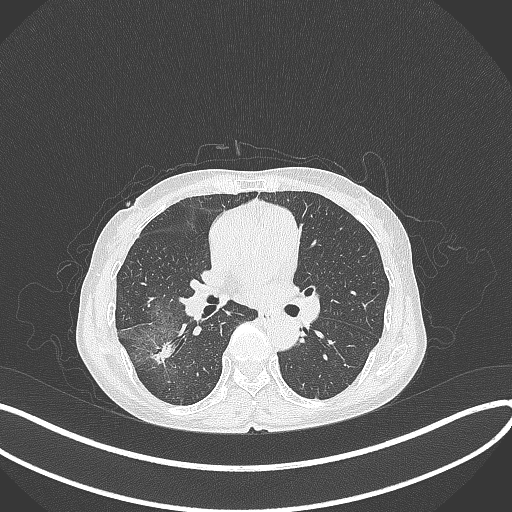
Chest CT, one axial slice. Slice 212 of 371 in the series (ordered by position). Reconstruction kernel B70f. 120 kVp. Lung window (W 1500 / L -600 HU). 1 mm slice thickness. 512 × 512 image matrix, field of view 400 × 400 mm. Patient: female, 69 years. From the clinical record (not read from this slice): clinical TNM (as recorded): T1b N0 M0; histopathological grade: G2-3.
Annotated regions visible in this slice (bounding box drawn by a radiologist):
- lung tumour (recorded histology: adenocarcinoma): box from (x=146, y=332) to (x=178, y=365) px